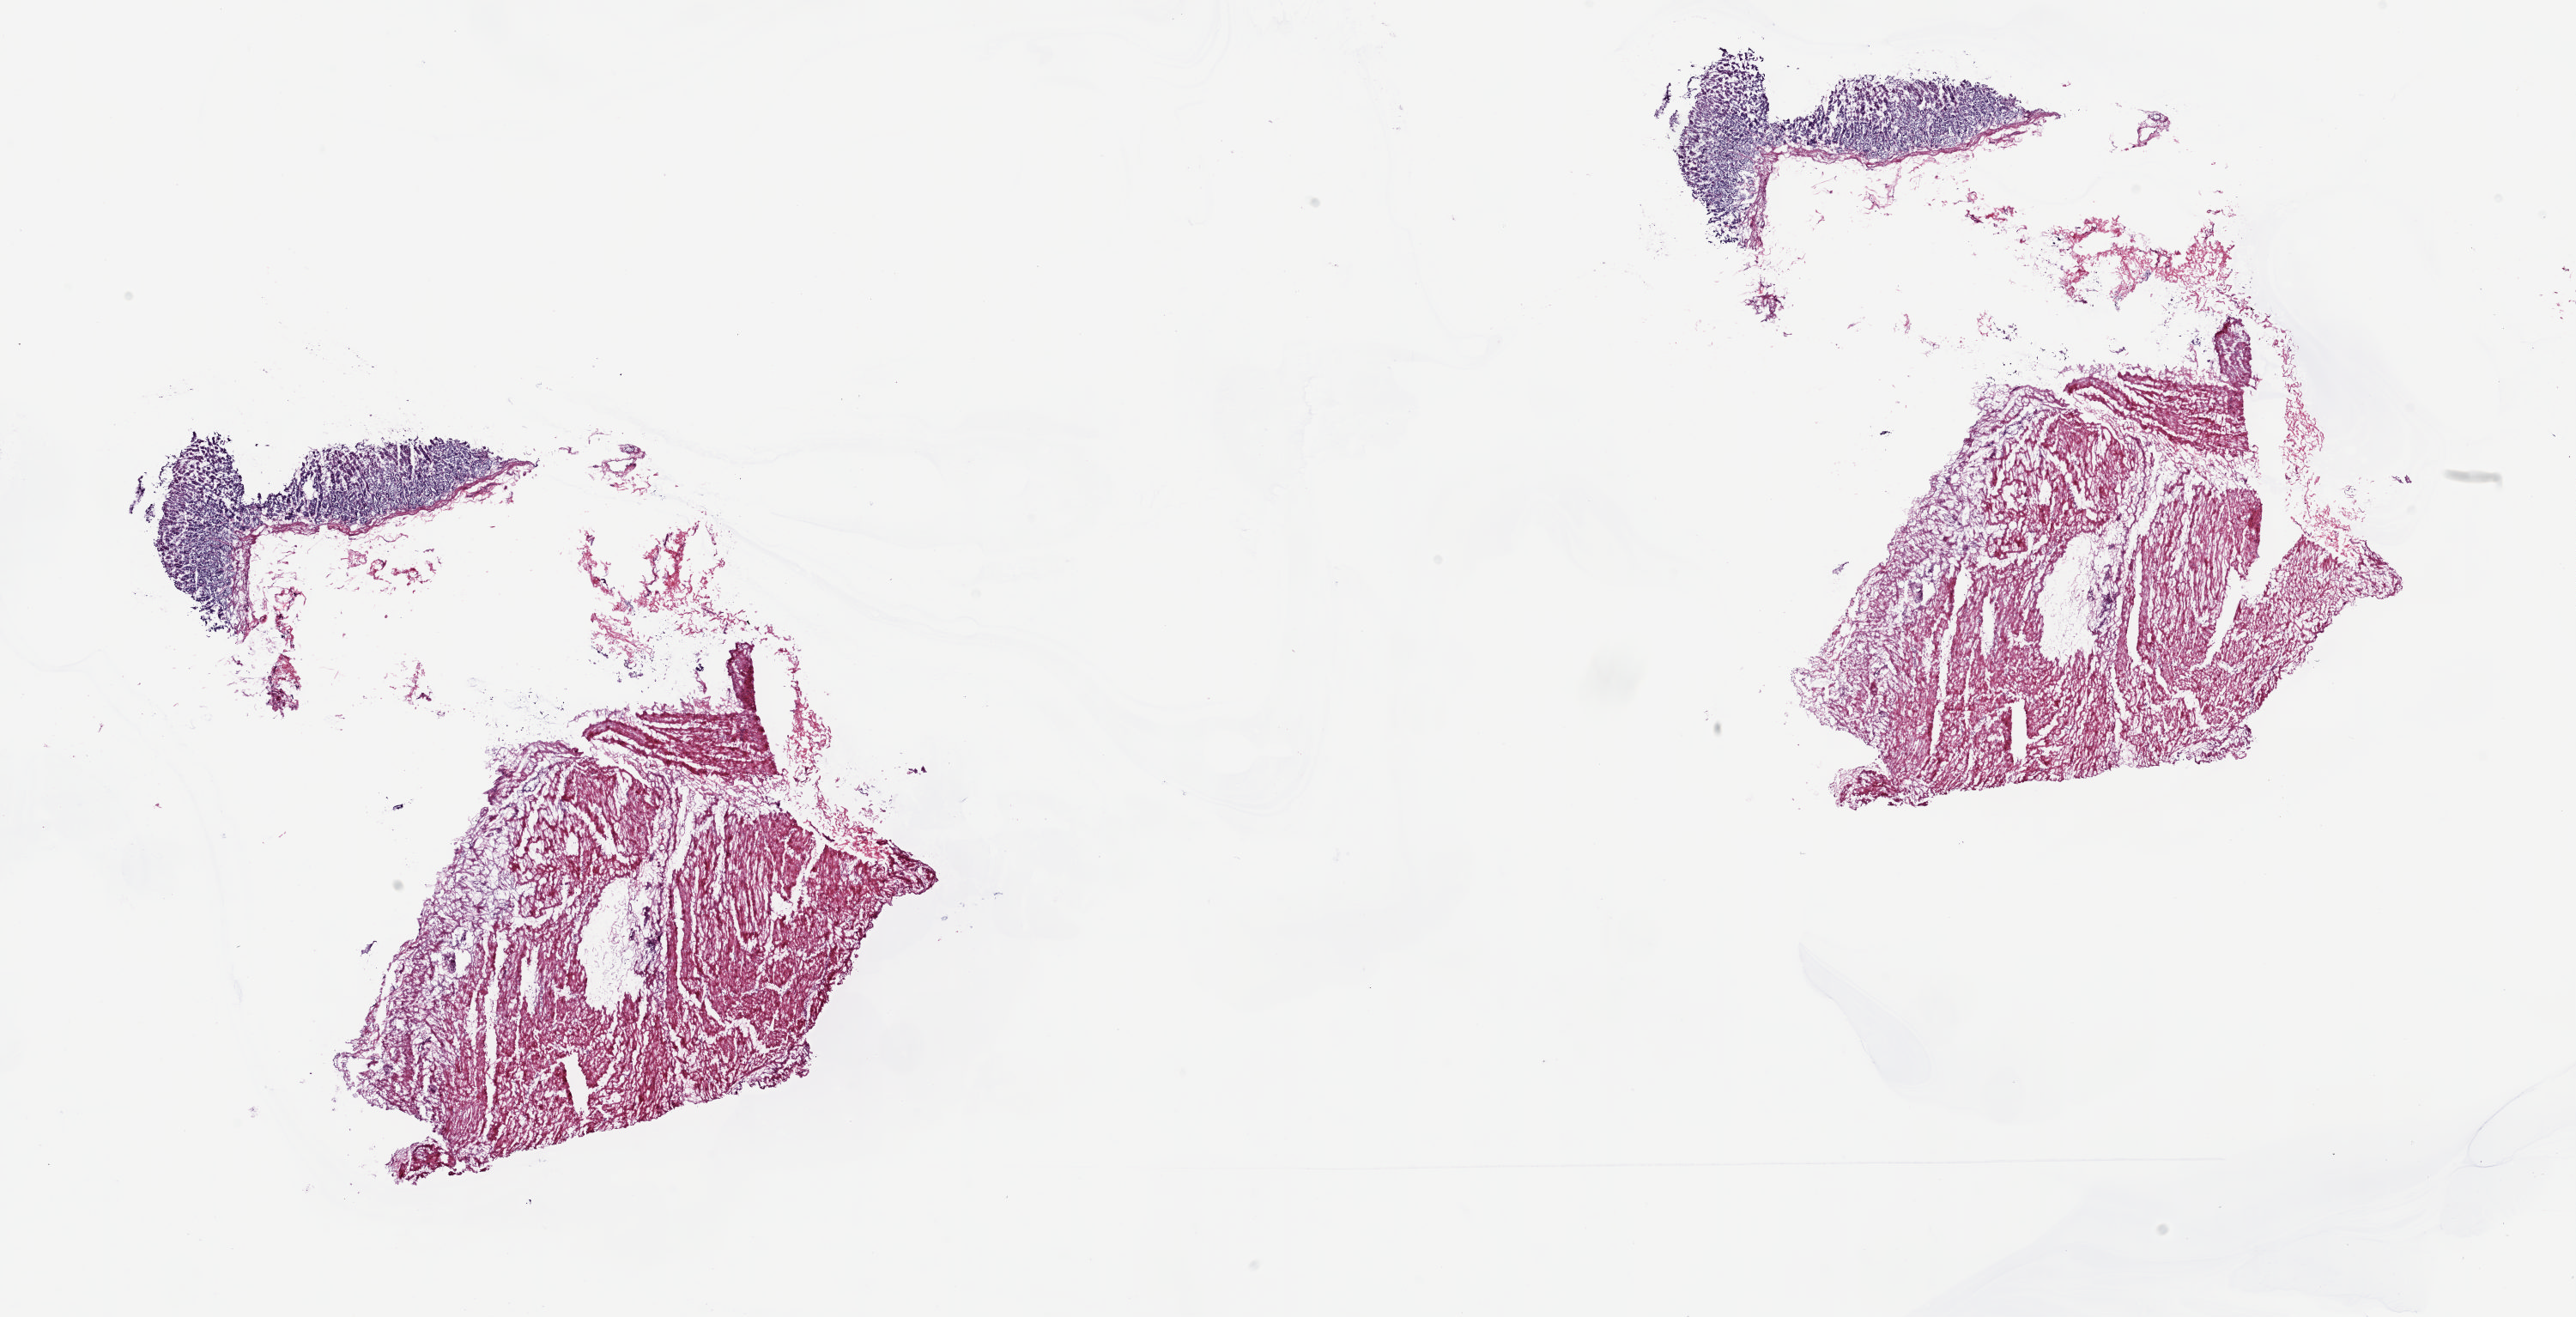
Digitized Hematoxylin and eosin (H&E) stained tissue section (whole slide) — low-resolution overview of the scanned area, about 23.8 x 12.2 mm; frozen section from the top of the tissue portion; esophagus, solid tissue normal (non-tumour tissue) sample. Male, age 74 years at initial diagnosis. Composition of this section per pathologist review: tumour cells 0%, tumour nuclei 0%, normal cells 15%, stromal cells 85%, necrosis 0%. Infiltration values recorded for this section: lymphocyte infiltration 15%, monocyte infiltration 1%, neutrophil infiltration 1%.
This section: solid tissue normal (non-tumour) sample from the same patient. Patient diagnosis: Adenocarcinoma, NOS (lower third of esophagus).